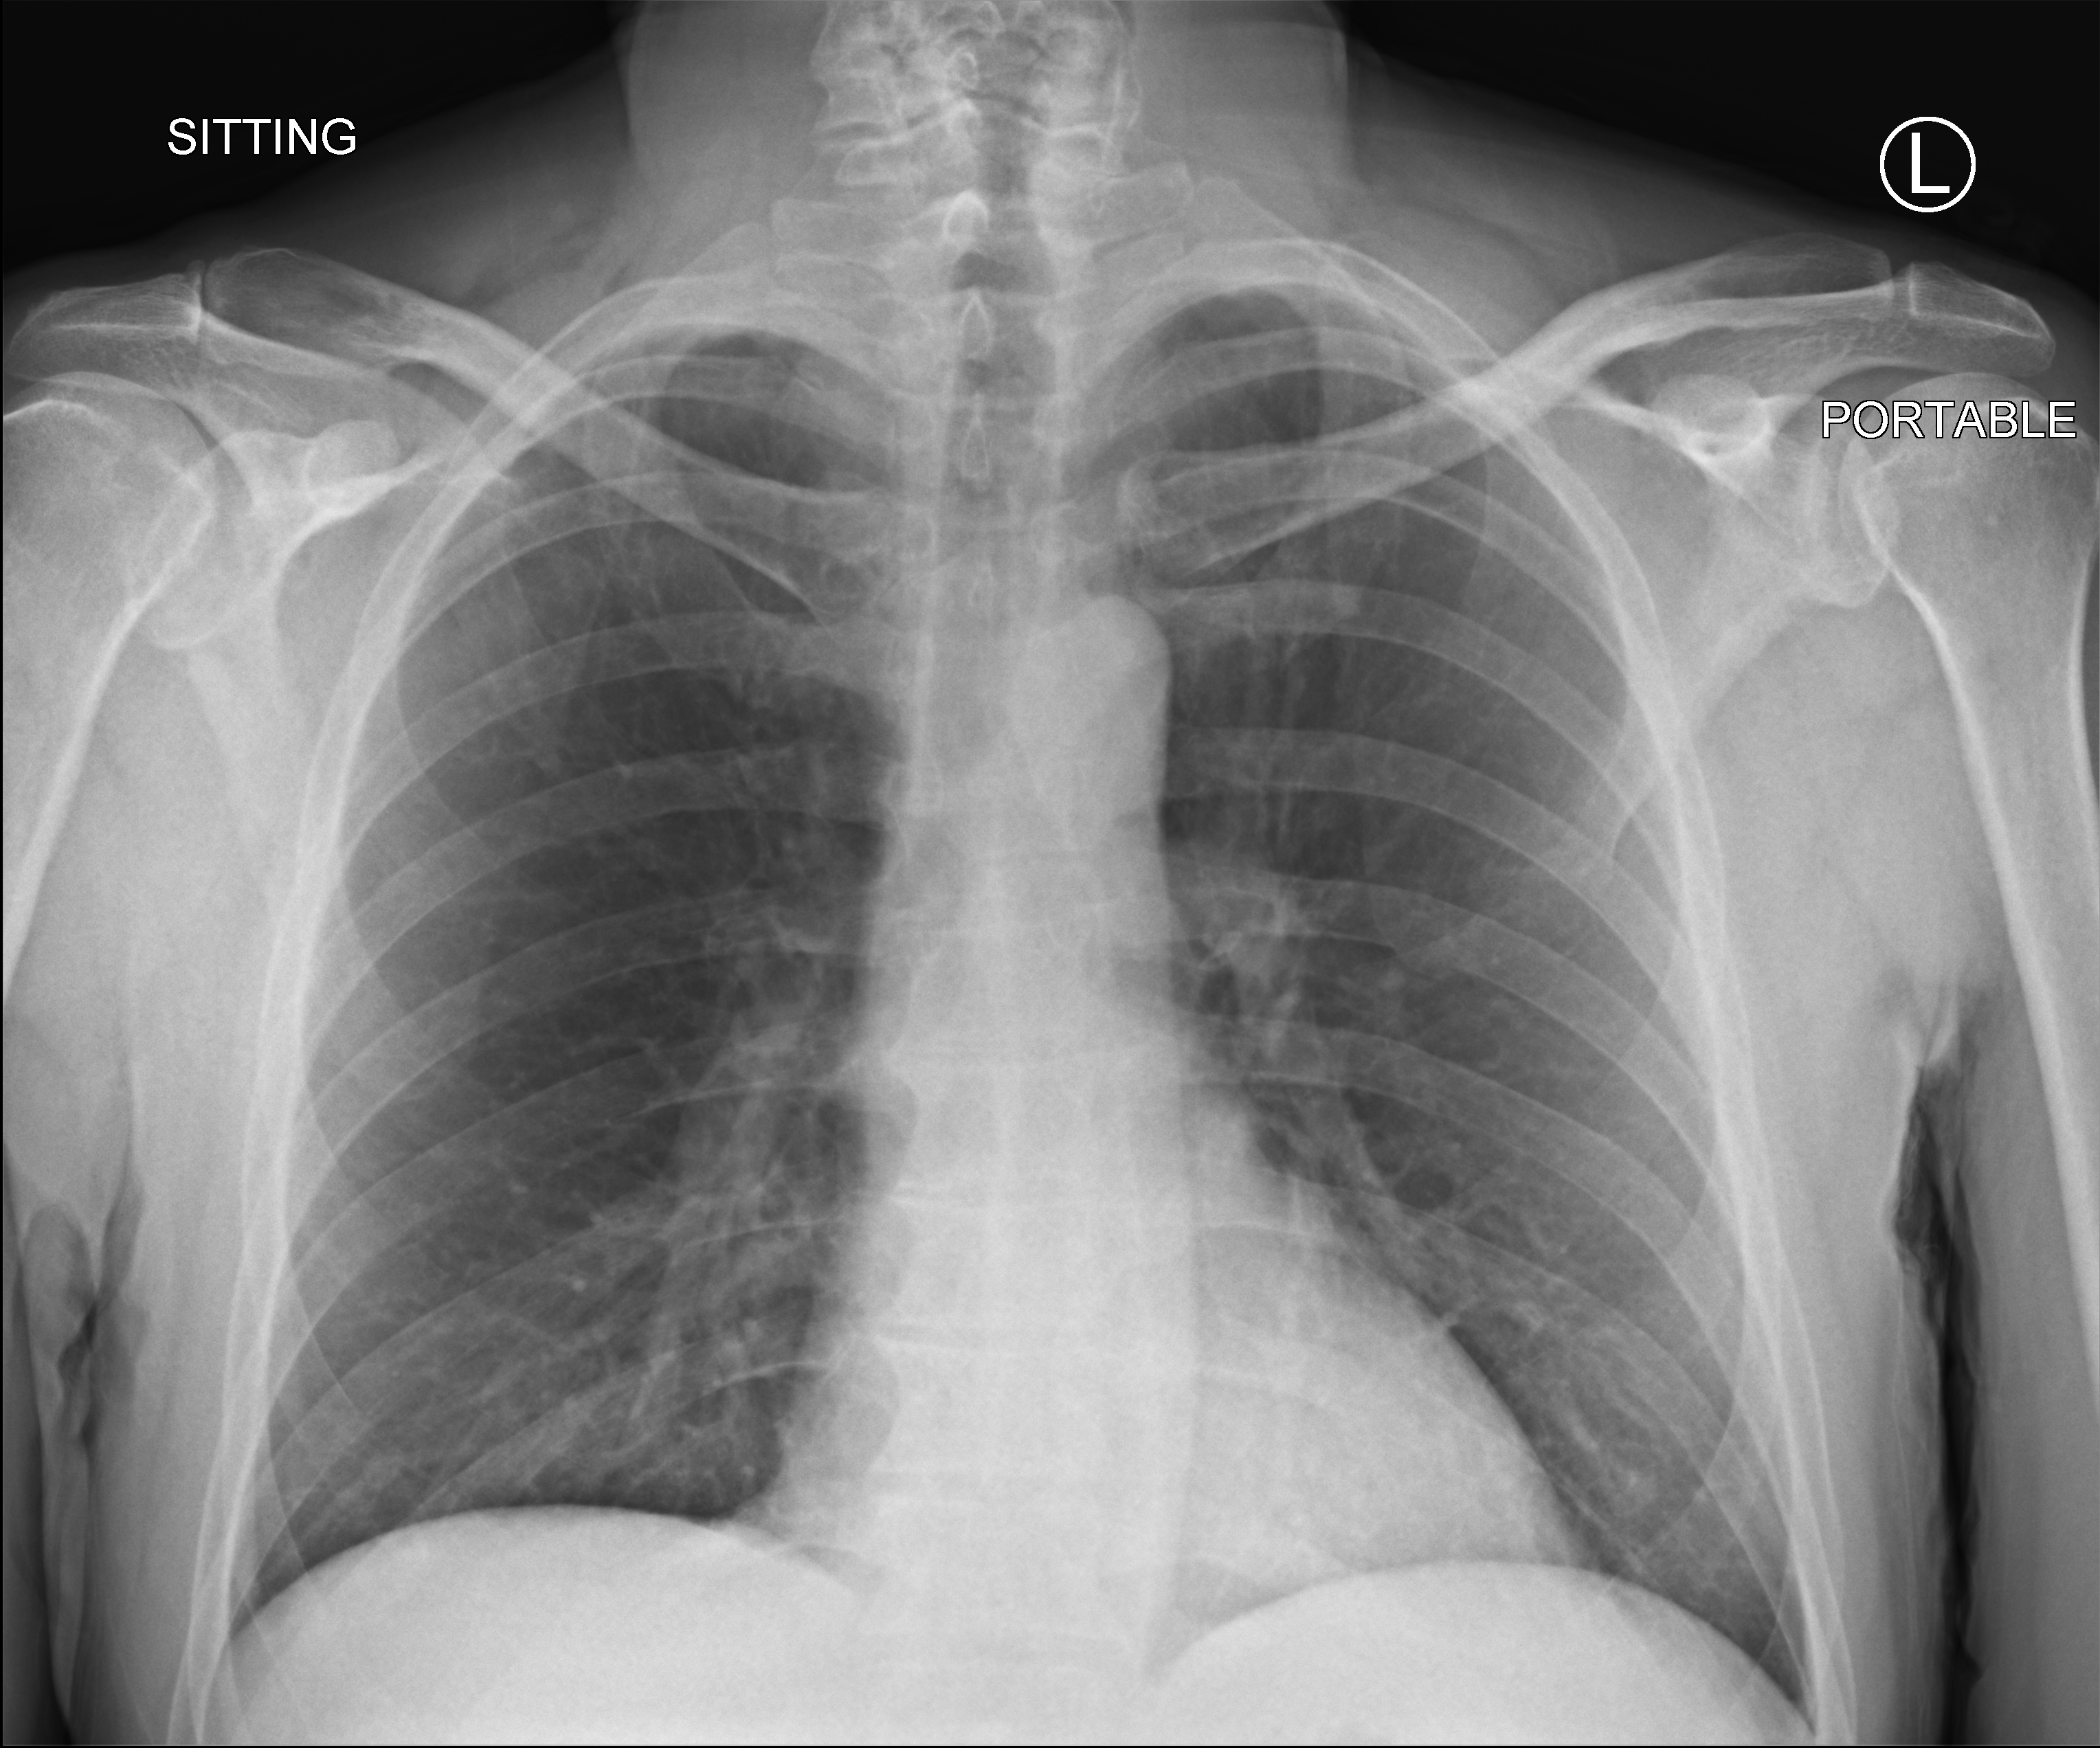
Portable chest radiograph, anteroposterior (AP) projection. Male patient hospitalised with COVID-19, age 18–59 years.
From the hospital-stay record, not from the radiograph (when in the stay this image was taken is not recorded):
- smoking status (admission record): never
- mechanically ventilated during this hospital stay: no